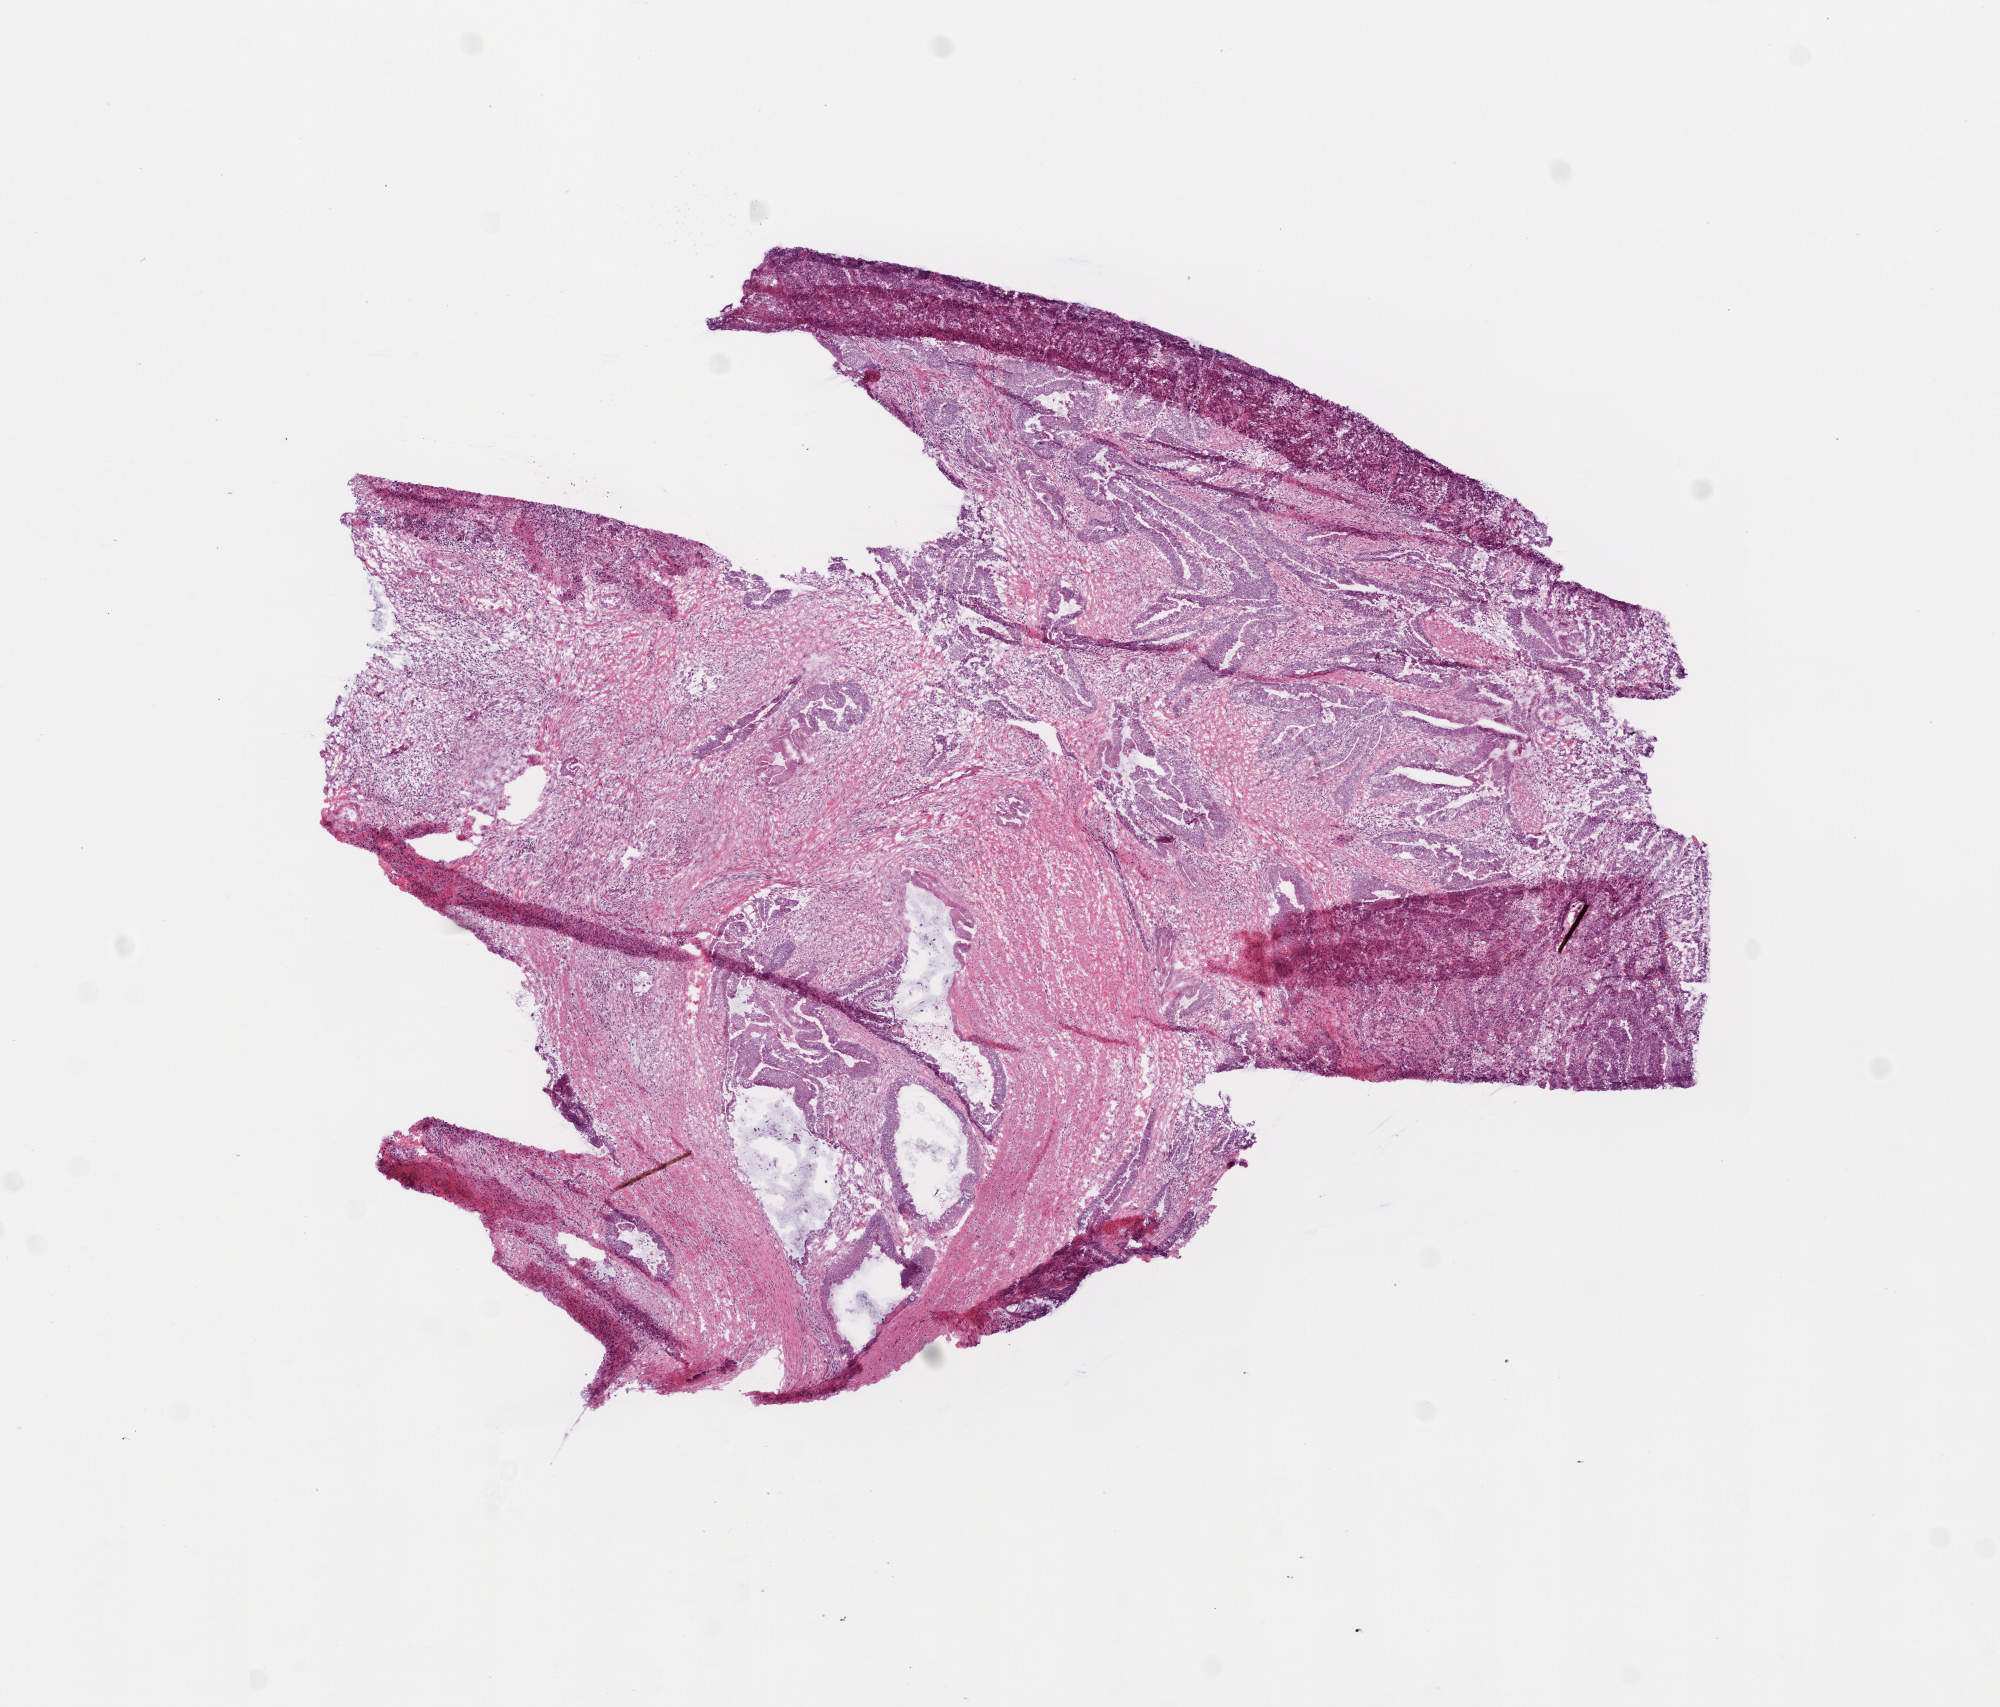
Whole-slide histology image, Hematoxylin and eosin (H&E) stained, a low-resolution overview of the entire scanned area, about 8.0 x 6.8 mm; frozen section from the top of the tissue portion; primary tumour sample from the colon. Male, age 67 years at initial diagnosis. Slide review estimates, as recorded: tumour cells 72%, tumour nuclei 75%, normal cells 0%, stromal cells 25%, necrosis 3%.
* AJCC pathologic stage: IIA
* histologic diagnosis: Mucinous adenocarcinoma
* lymph nodes positive (case pathology): 0 of 36 examined
* TNM: T3 N0 M0